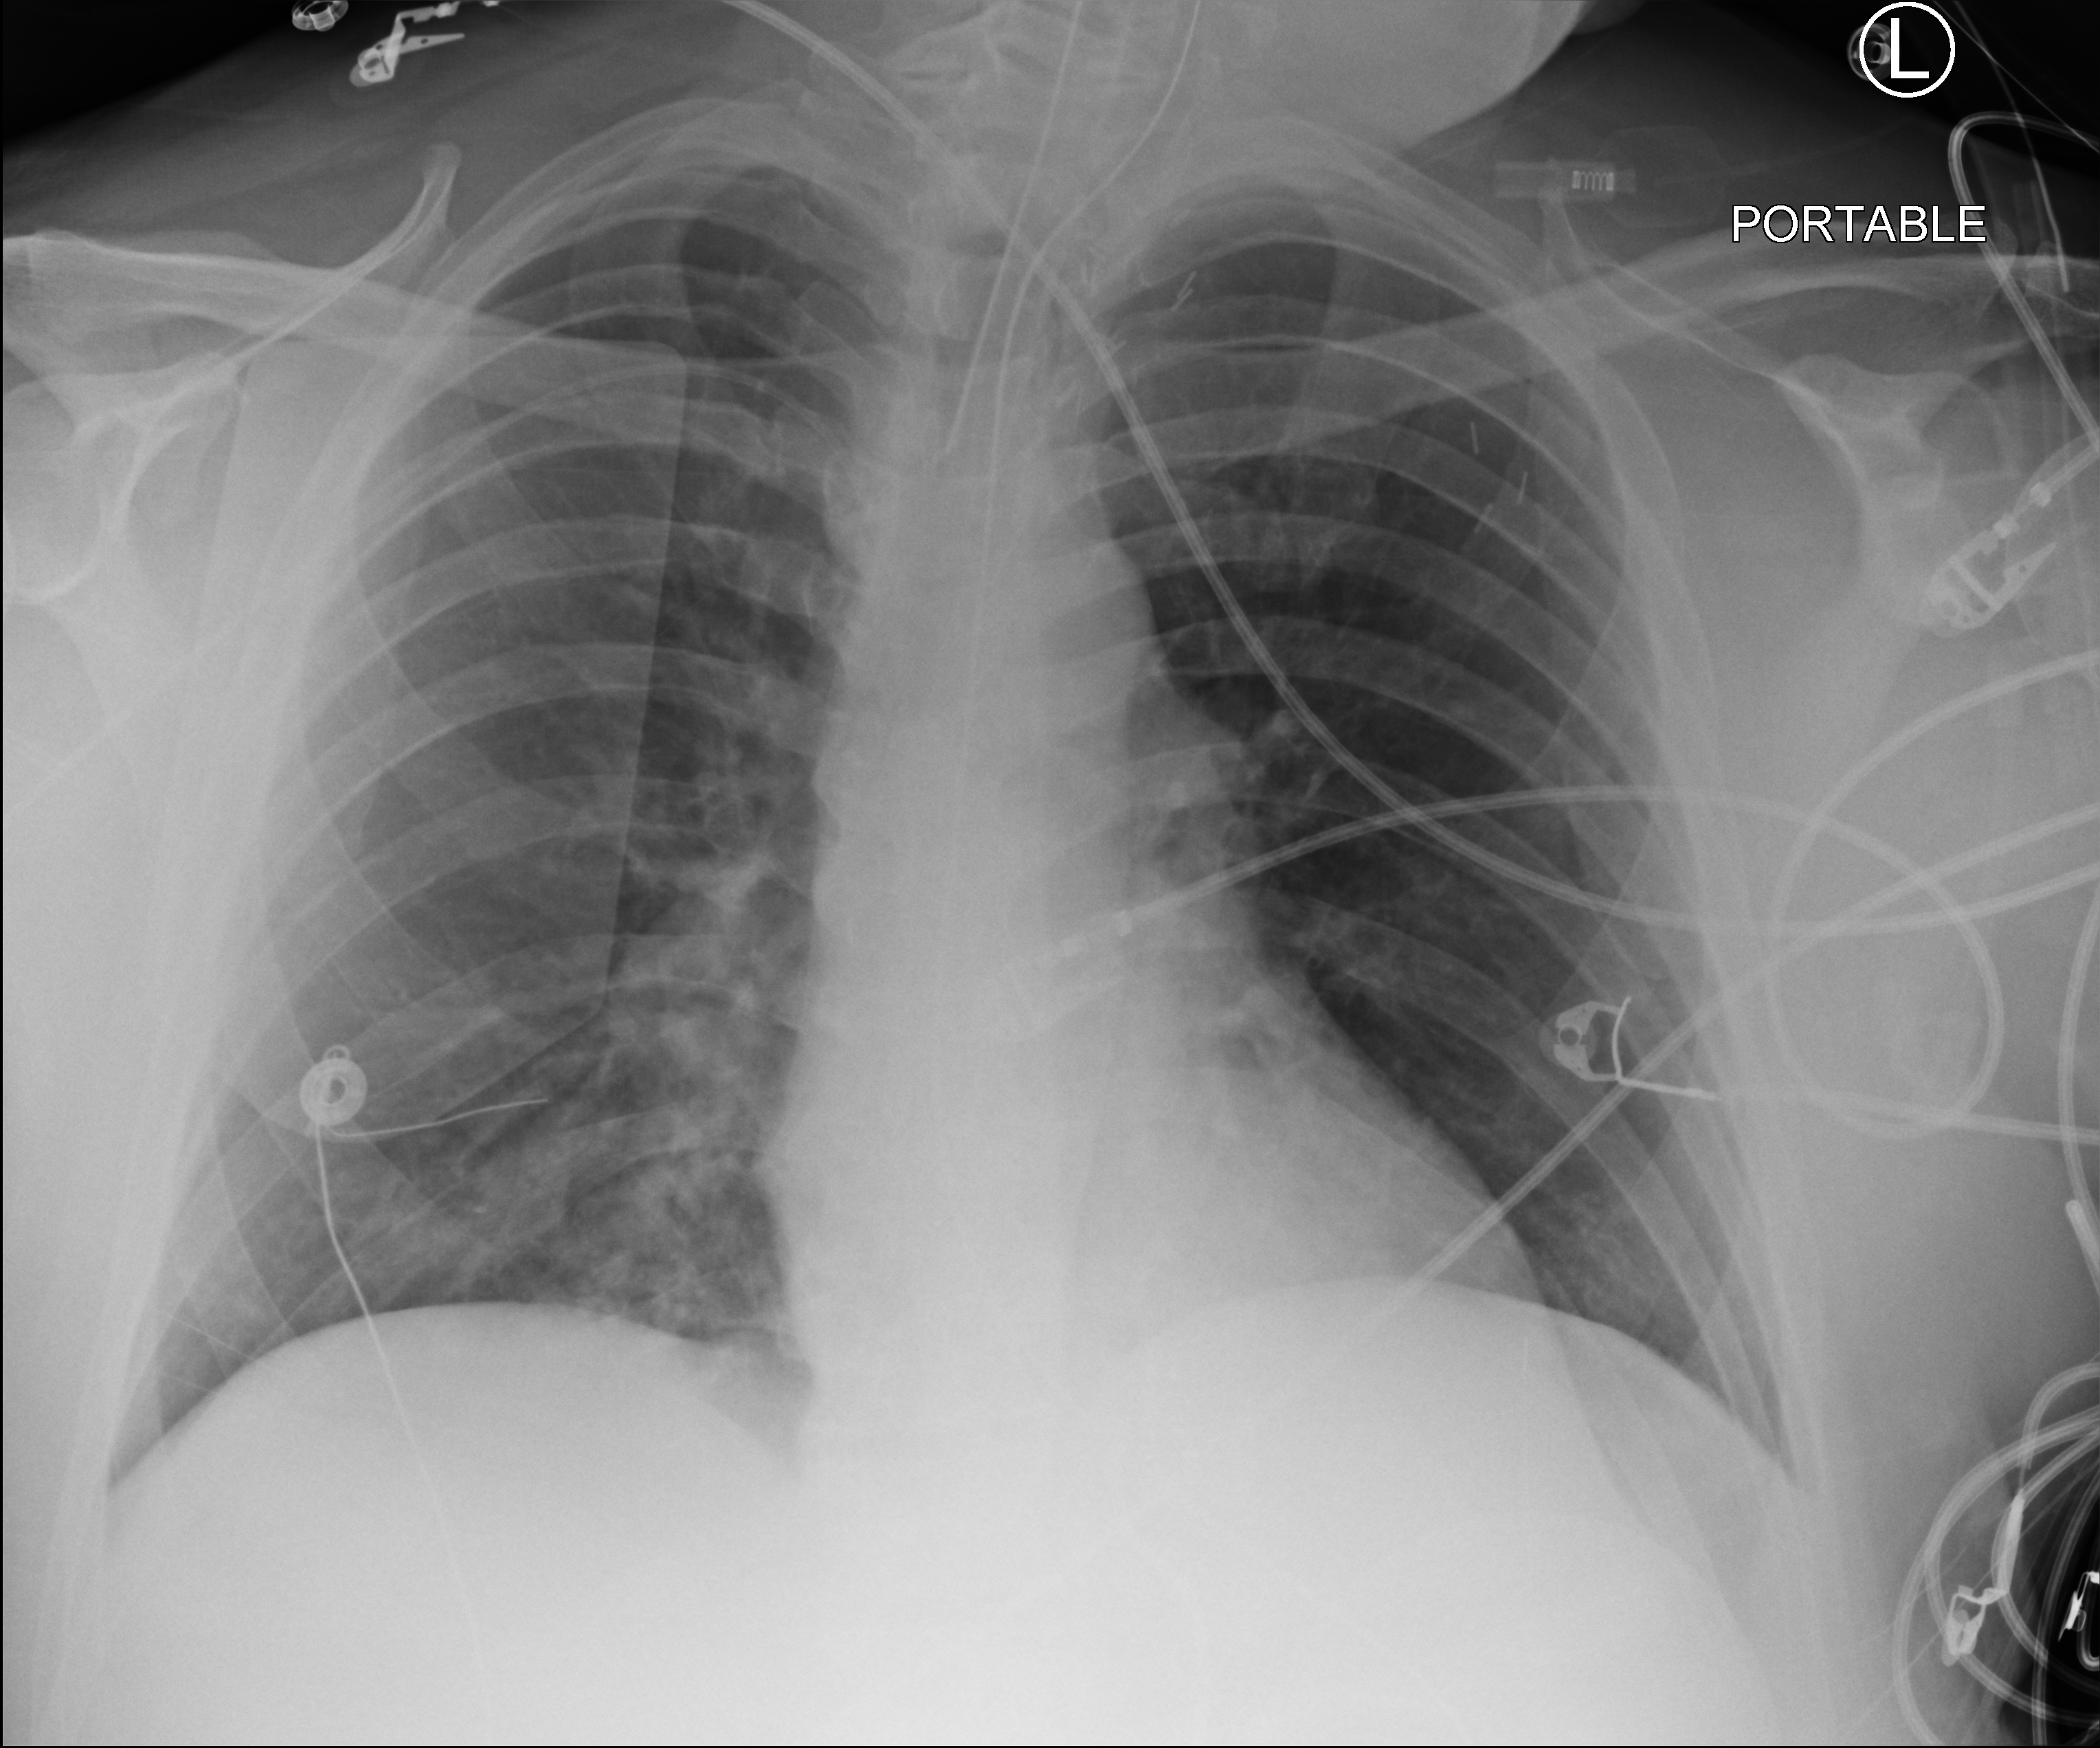
Bedside chest radiograph (computed radiography); anteroposterior (AP) projection. Adult patient hospitalised with COVID-19, age 18–59 years.
From the hospital-stay record, not from the radiograph (when in the stay this image was taken is not recorded): chronic kidney disease (admission record): yes; mechanically ventilated during this hospital stay: yes; other chronic lung disease (admission record): no.